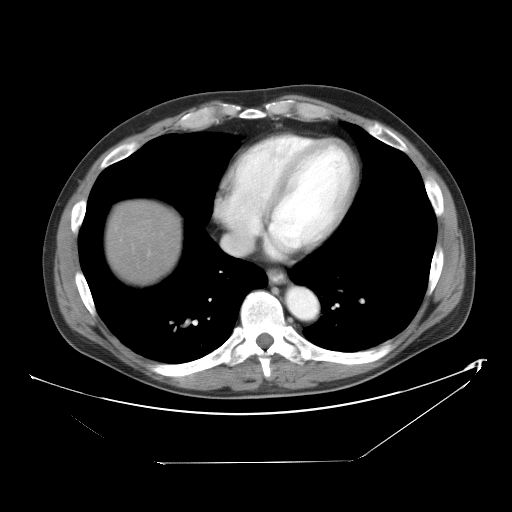
Contrast-enhanced abdominal CT, one axial slice. Position 50 of 53 along the scan axis. Reconstruction kernel STANDARD. Intravenous contrast given. Soft-tissue window (W 400 / L 40 HU). 512 × 512 image matrix. Male patient, age 59 years. Case-level facts recorded for this patient, not image findings: diagnosis: colorectal cancer liver metastases, imaged before liver resection; multiple liver metastases: yes.
Structures marked on this image (outlined manually by an expert reader):
- liver: bounding box (x1, y1, x2, y2) in pixels: (110, 204, 179, 281)
- planned liver remnant (the part of the liver to remain after resection): (109, 204, 178, 281)